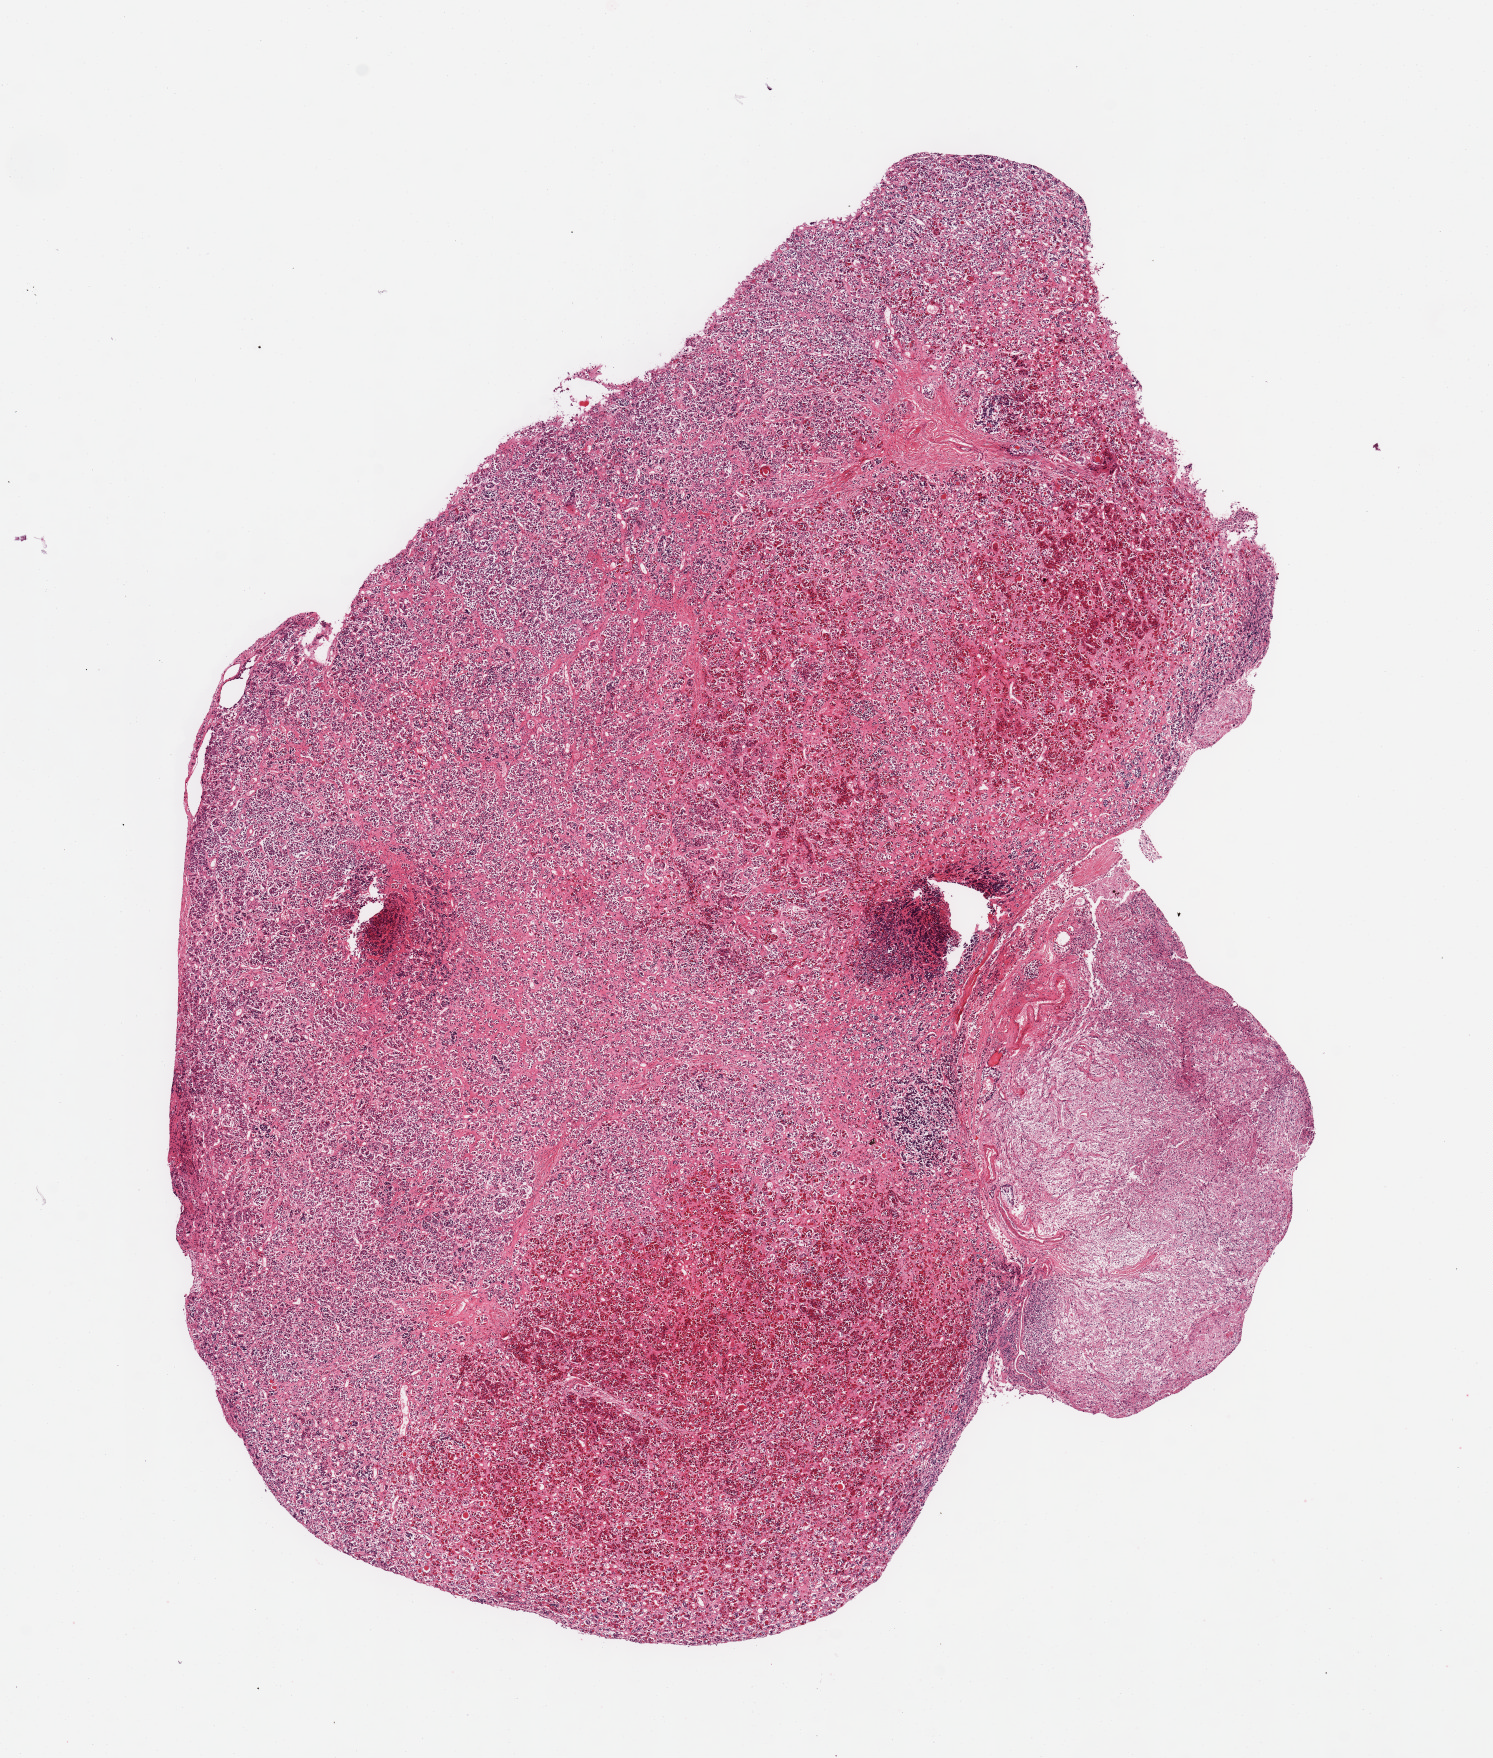
Whole-slide image, H&E stain — low-resolution overview of the scanned area, about 11.8 x 13.9 mm, PAXgene-fixed, paraffin-embedded tissue, section of pituitary (target tissue), tissue donor sample. Donor: male.
- pathologist's review note for this sample: 1 piece, mainly adenohypophysis, moderately autolyzed; 4x2mm portion of neurohypophysis